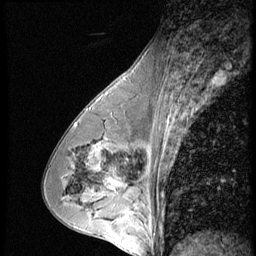
Breast MRI (dynamic contrast-enhanced), one sagittal slice. Slice 30 of 56 in the series (ordered by position). 3 images stored at this slice position (order not interpretable as contrast timing). 1.5 T. TE 4.2 ms, TR 9 ms. 2.5 mm slice thickness. 256 × 256 image matrix. Female patient, age 43 years. Case-level facts recorded for this patient, not image findings: setting: breast cancer imaged before/during neoadjuvant chemotherapy; receptor status: HR-positive, HER2-negative.
Structures marked on this image (semi-automatic segmentation, software-assisted and operator-edited):
- analysis volume of interest (the breast-tissue region the enhancement analysis was run in; not a lesion): bounding box [x1, y1, x2, y2] px = [120, 160, 163, 207]
- tumour enhancement mask (voxels above the 140 % enhancement threshold inside the analysis volume of interest): [120, 192, 130, 207]